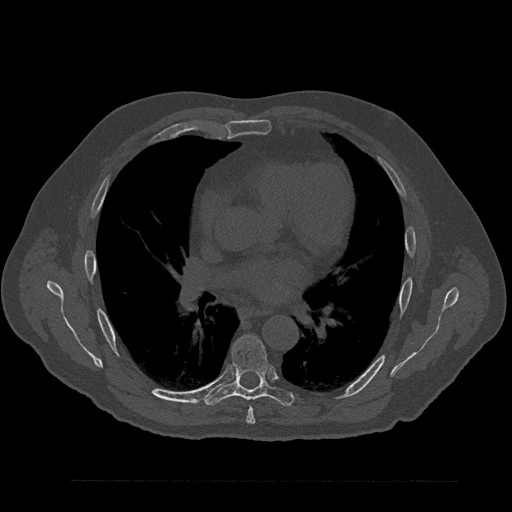
CT including the spine, one axial slice; slice 517 of 797 in the series (ordered by position); reconstruction kernel Br40s/3; 120 kVp; bone window (W 1800 / L 400 HU); 512 × 512 image matrix, field of view 430 × 430 mm. Male patient, age 61 years. From the clinical record (not read from this slice): primary cancer: prostate.
Annotated regions visible in this slice (semi-automatic segmentation, software-assisted and operator-edited):
- T6 vertebra: bounding box (x1, y1, x2, y2) in pixels: (246, 408, 256, 424)
- T7 vertebra: (204, 335, 294, 406)